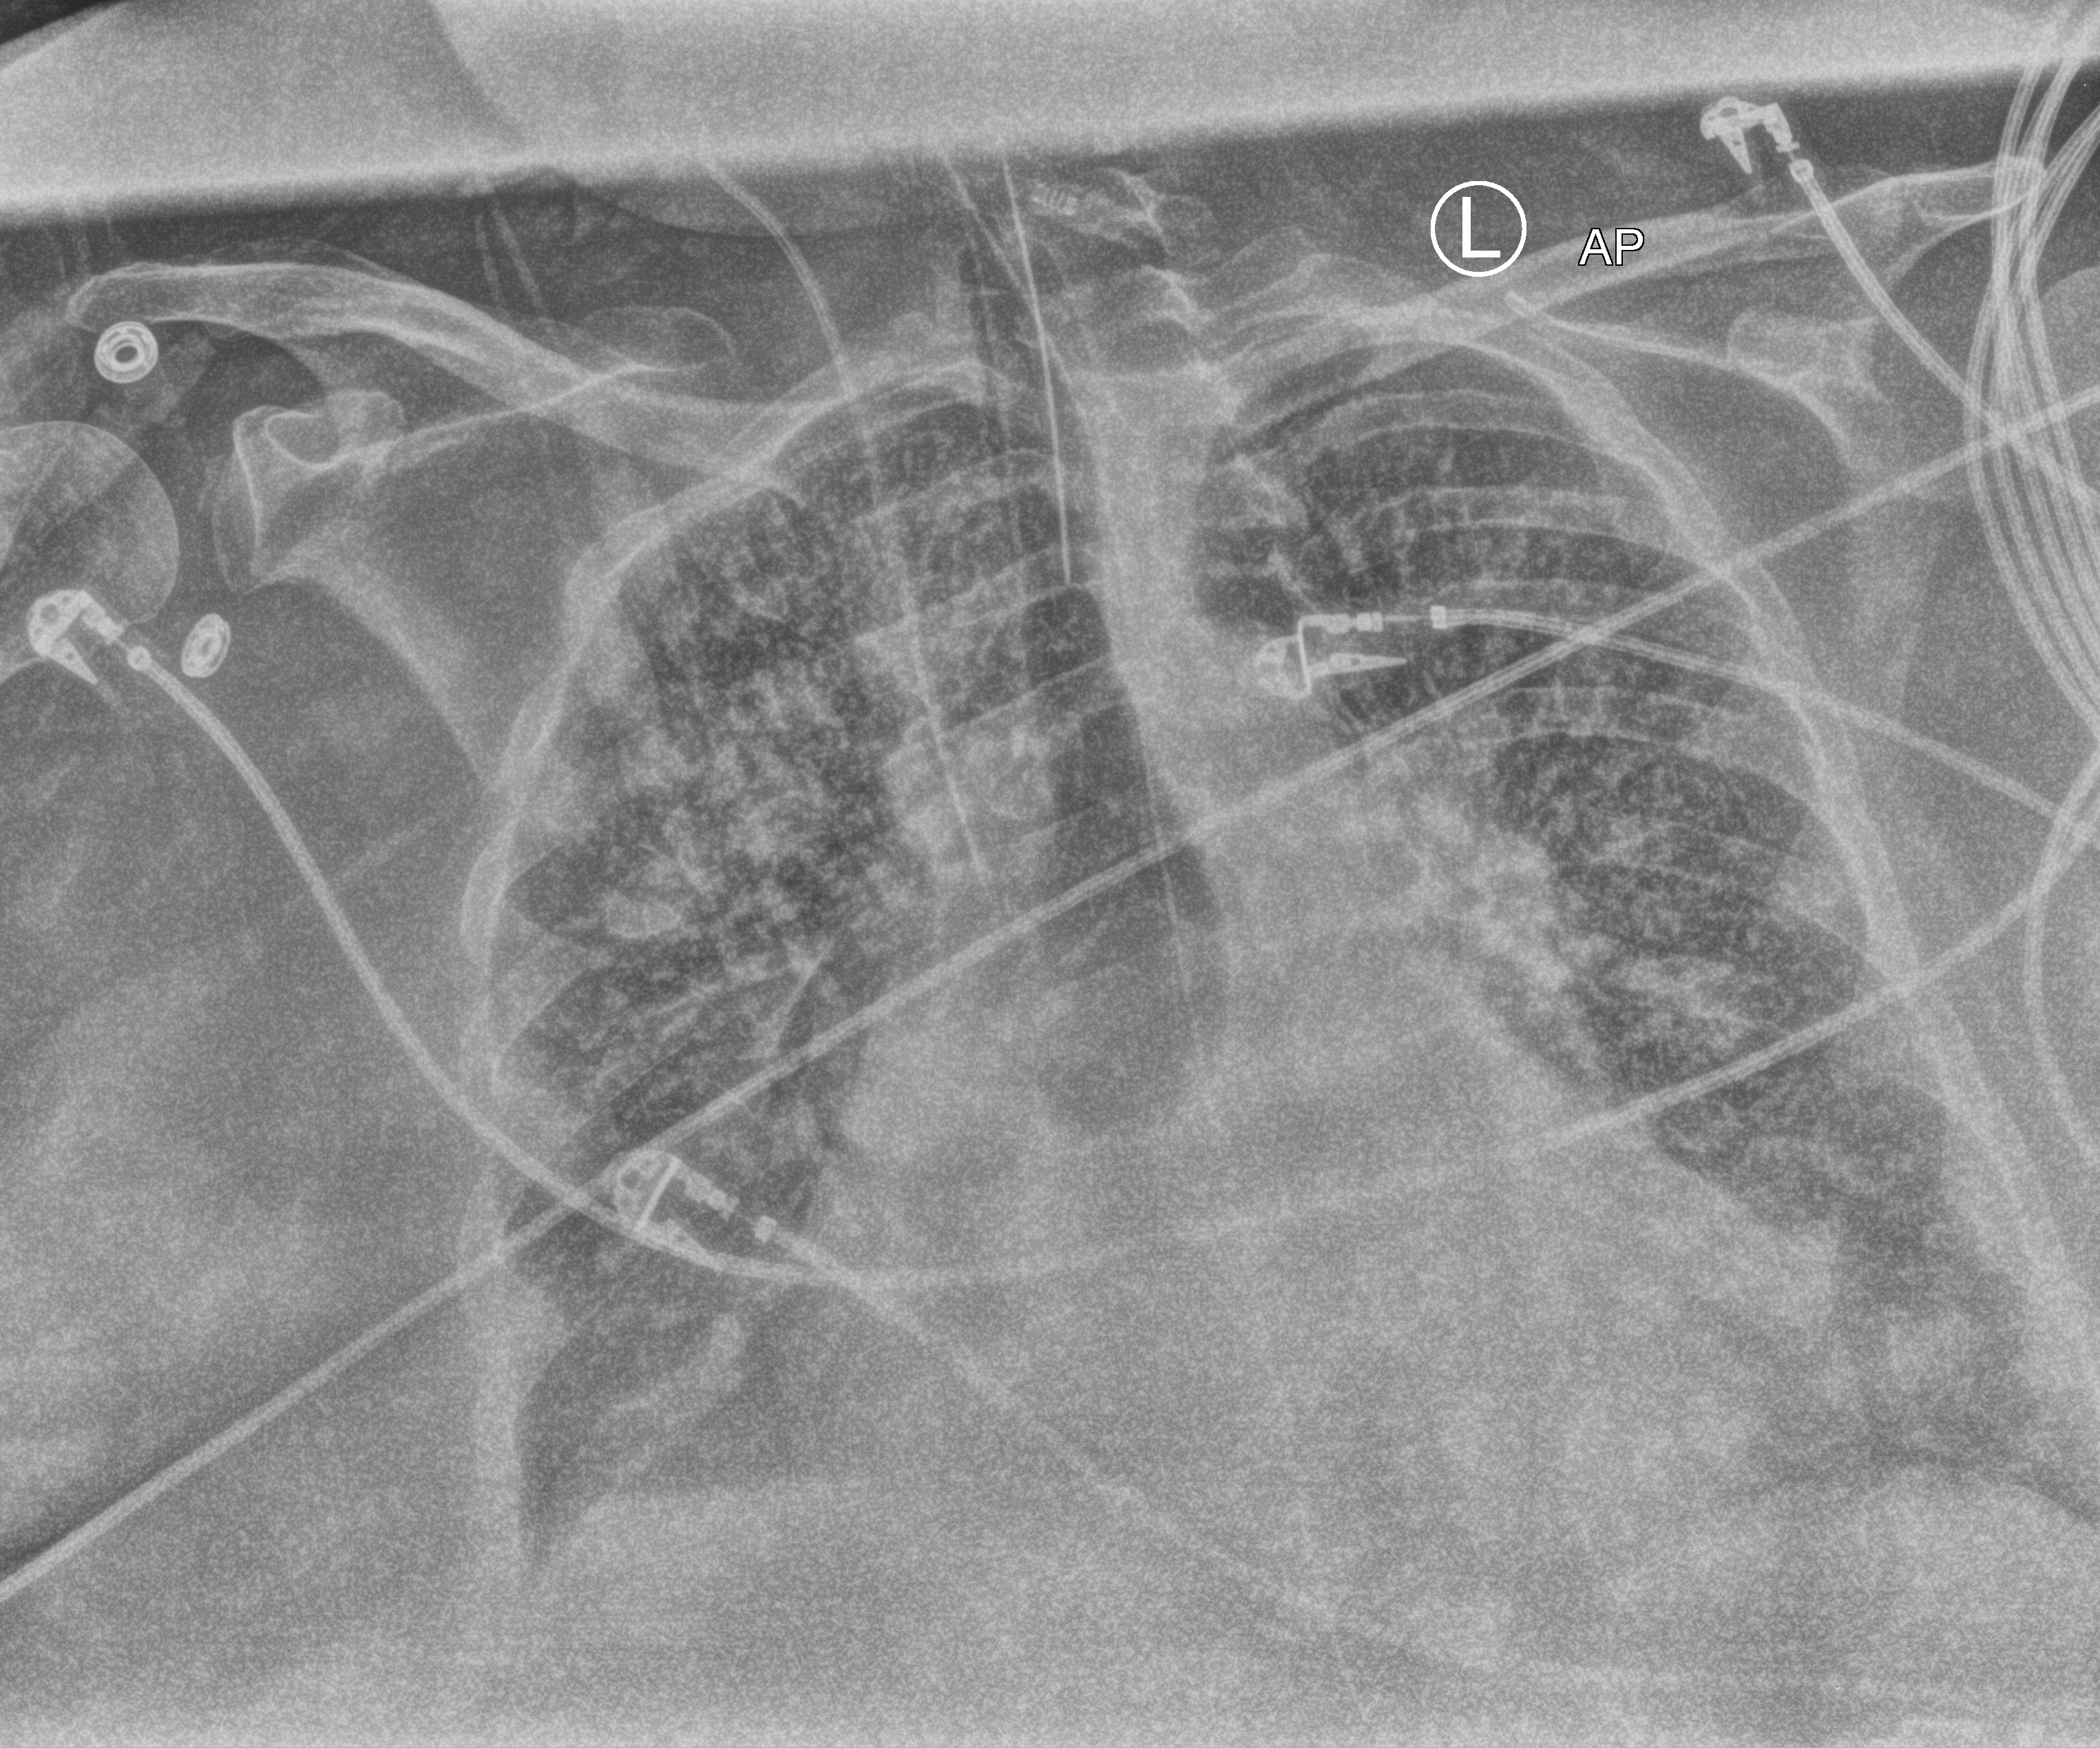
Chest X-ray (portable); anteroposterior (AP) projection. Female patient hospitalised with COVID-19, age 60–74 years.
Admission-level facts for this patient (not findings on this image; timing relative to this image not recorded):
- length of hospital stay: 6 days
- hypertension (admission record): yes